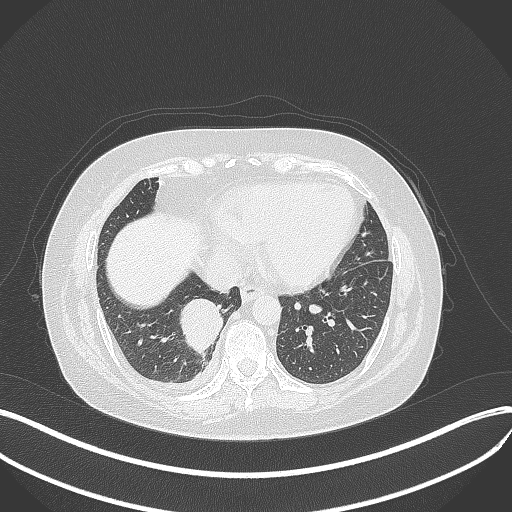
Chest CT, one axial slice; slice 114 of 381 in the series (ordered by position); 120 kVp; lung window (W 1500 / L -600 HU); 1 mm slice thickness; 512 × 512 image matrix, field of view 400 × 400 mm. Patient: female, 56 years. Case-level facts recorded for this patient, not image findings: clinical TNM (as recorded): T2b N1 M0; histopathological grade: G3.
Structures marked on this image (bounding box drawn by a radiologist):
- lung tumour (recorded histology: small cell carcinoma): box from (x=180, y=295) to (x=225, y=353) px